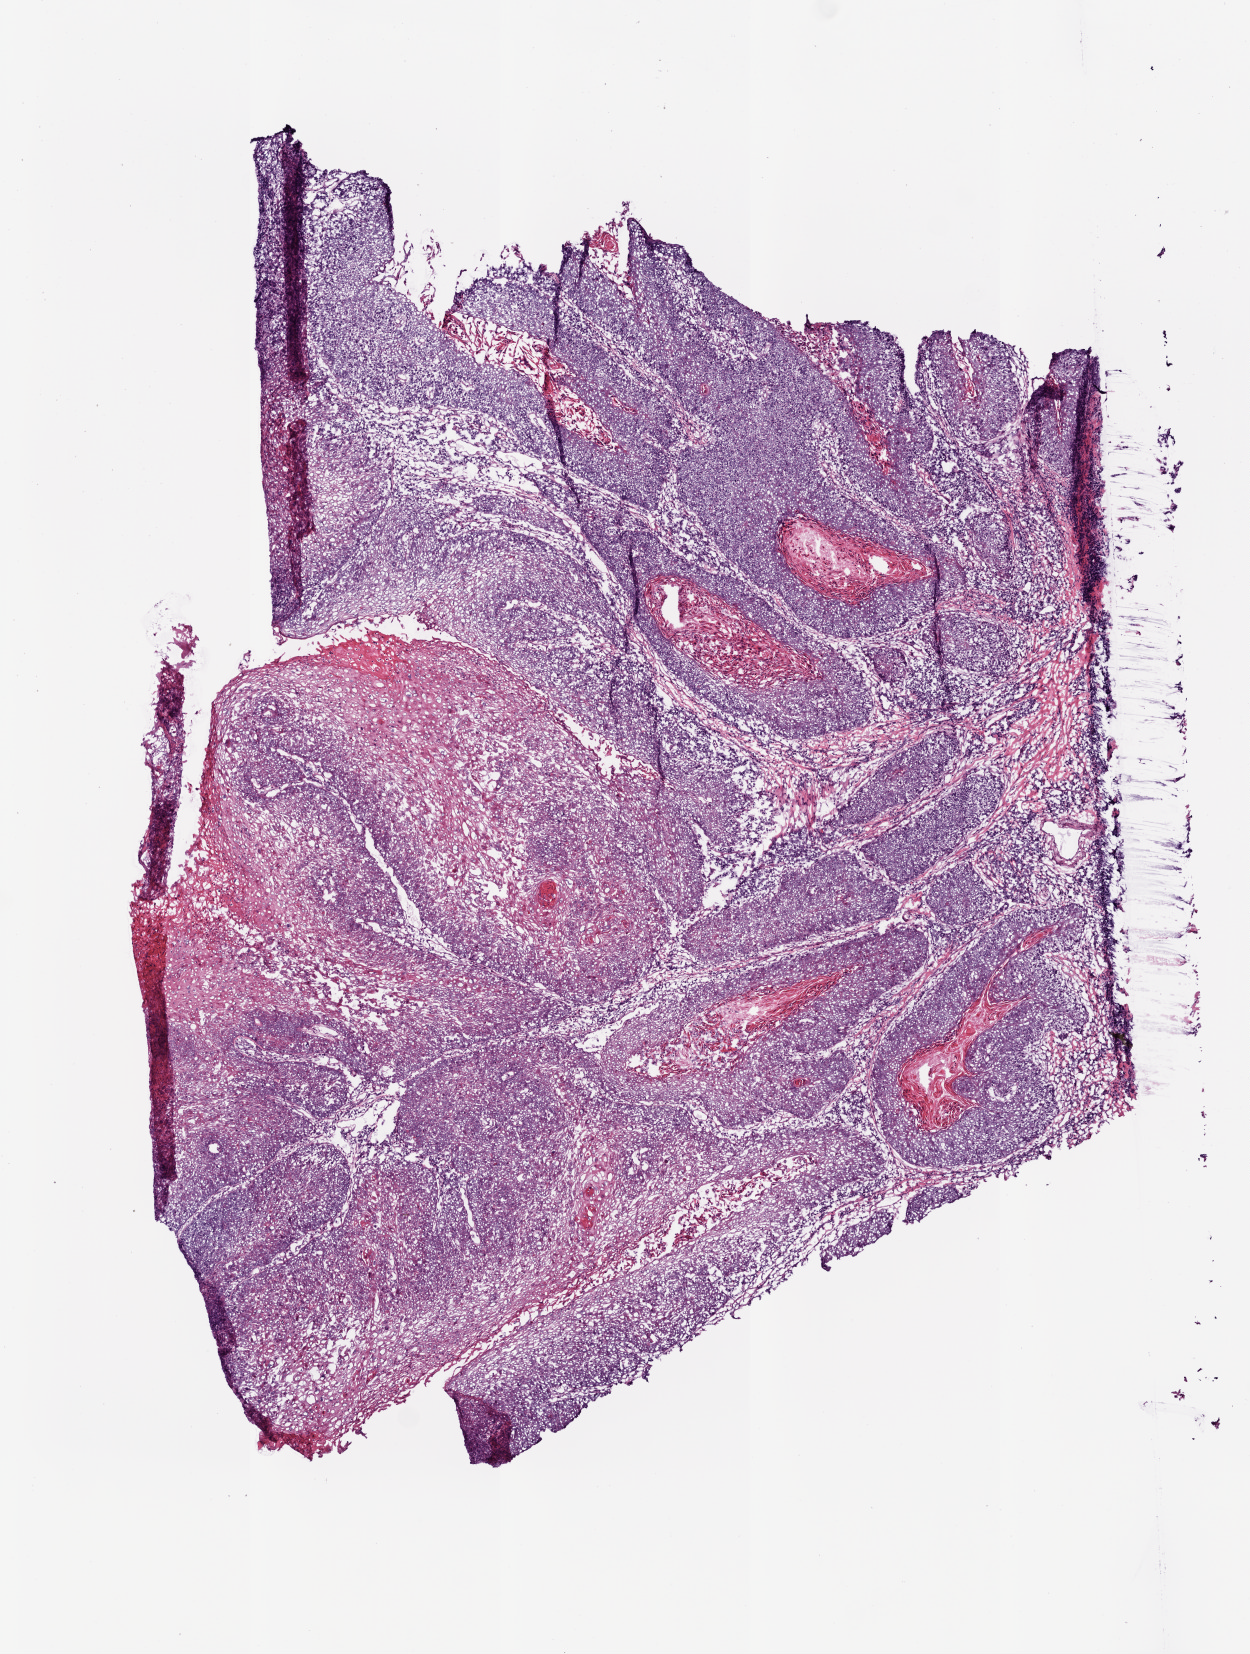
Digitized Hematoxylin and eosin (H&E) stained tissue section (whole slide), shown as a low-resolution overview of the whole scanned area (about 5.0 x 6.6 mm), frozen section from the bottom of the tissue portion, primary tumour sample from the head and neck. Patient: male, age at initial diagnosis 82 years. Histologic grade: G2 (moderately differentiated). Pathologist review of this section (percent, as recorded): tumour cells 96%, tumour nuclei 80%, normal cells 0%, stromal cells 1%, necrosis 5%. Infiltration values recorded for this section: lymphocyte infiltration 10%, neutrophil infiltration 1%.
* AJCC pathologic stage: I (6th edition)
* histologic diagnosis: Squamous cell carcinoma, NOS (overlapping lesion of lip, oral cavity and pharynx)